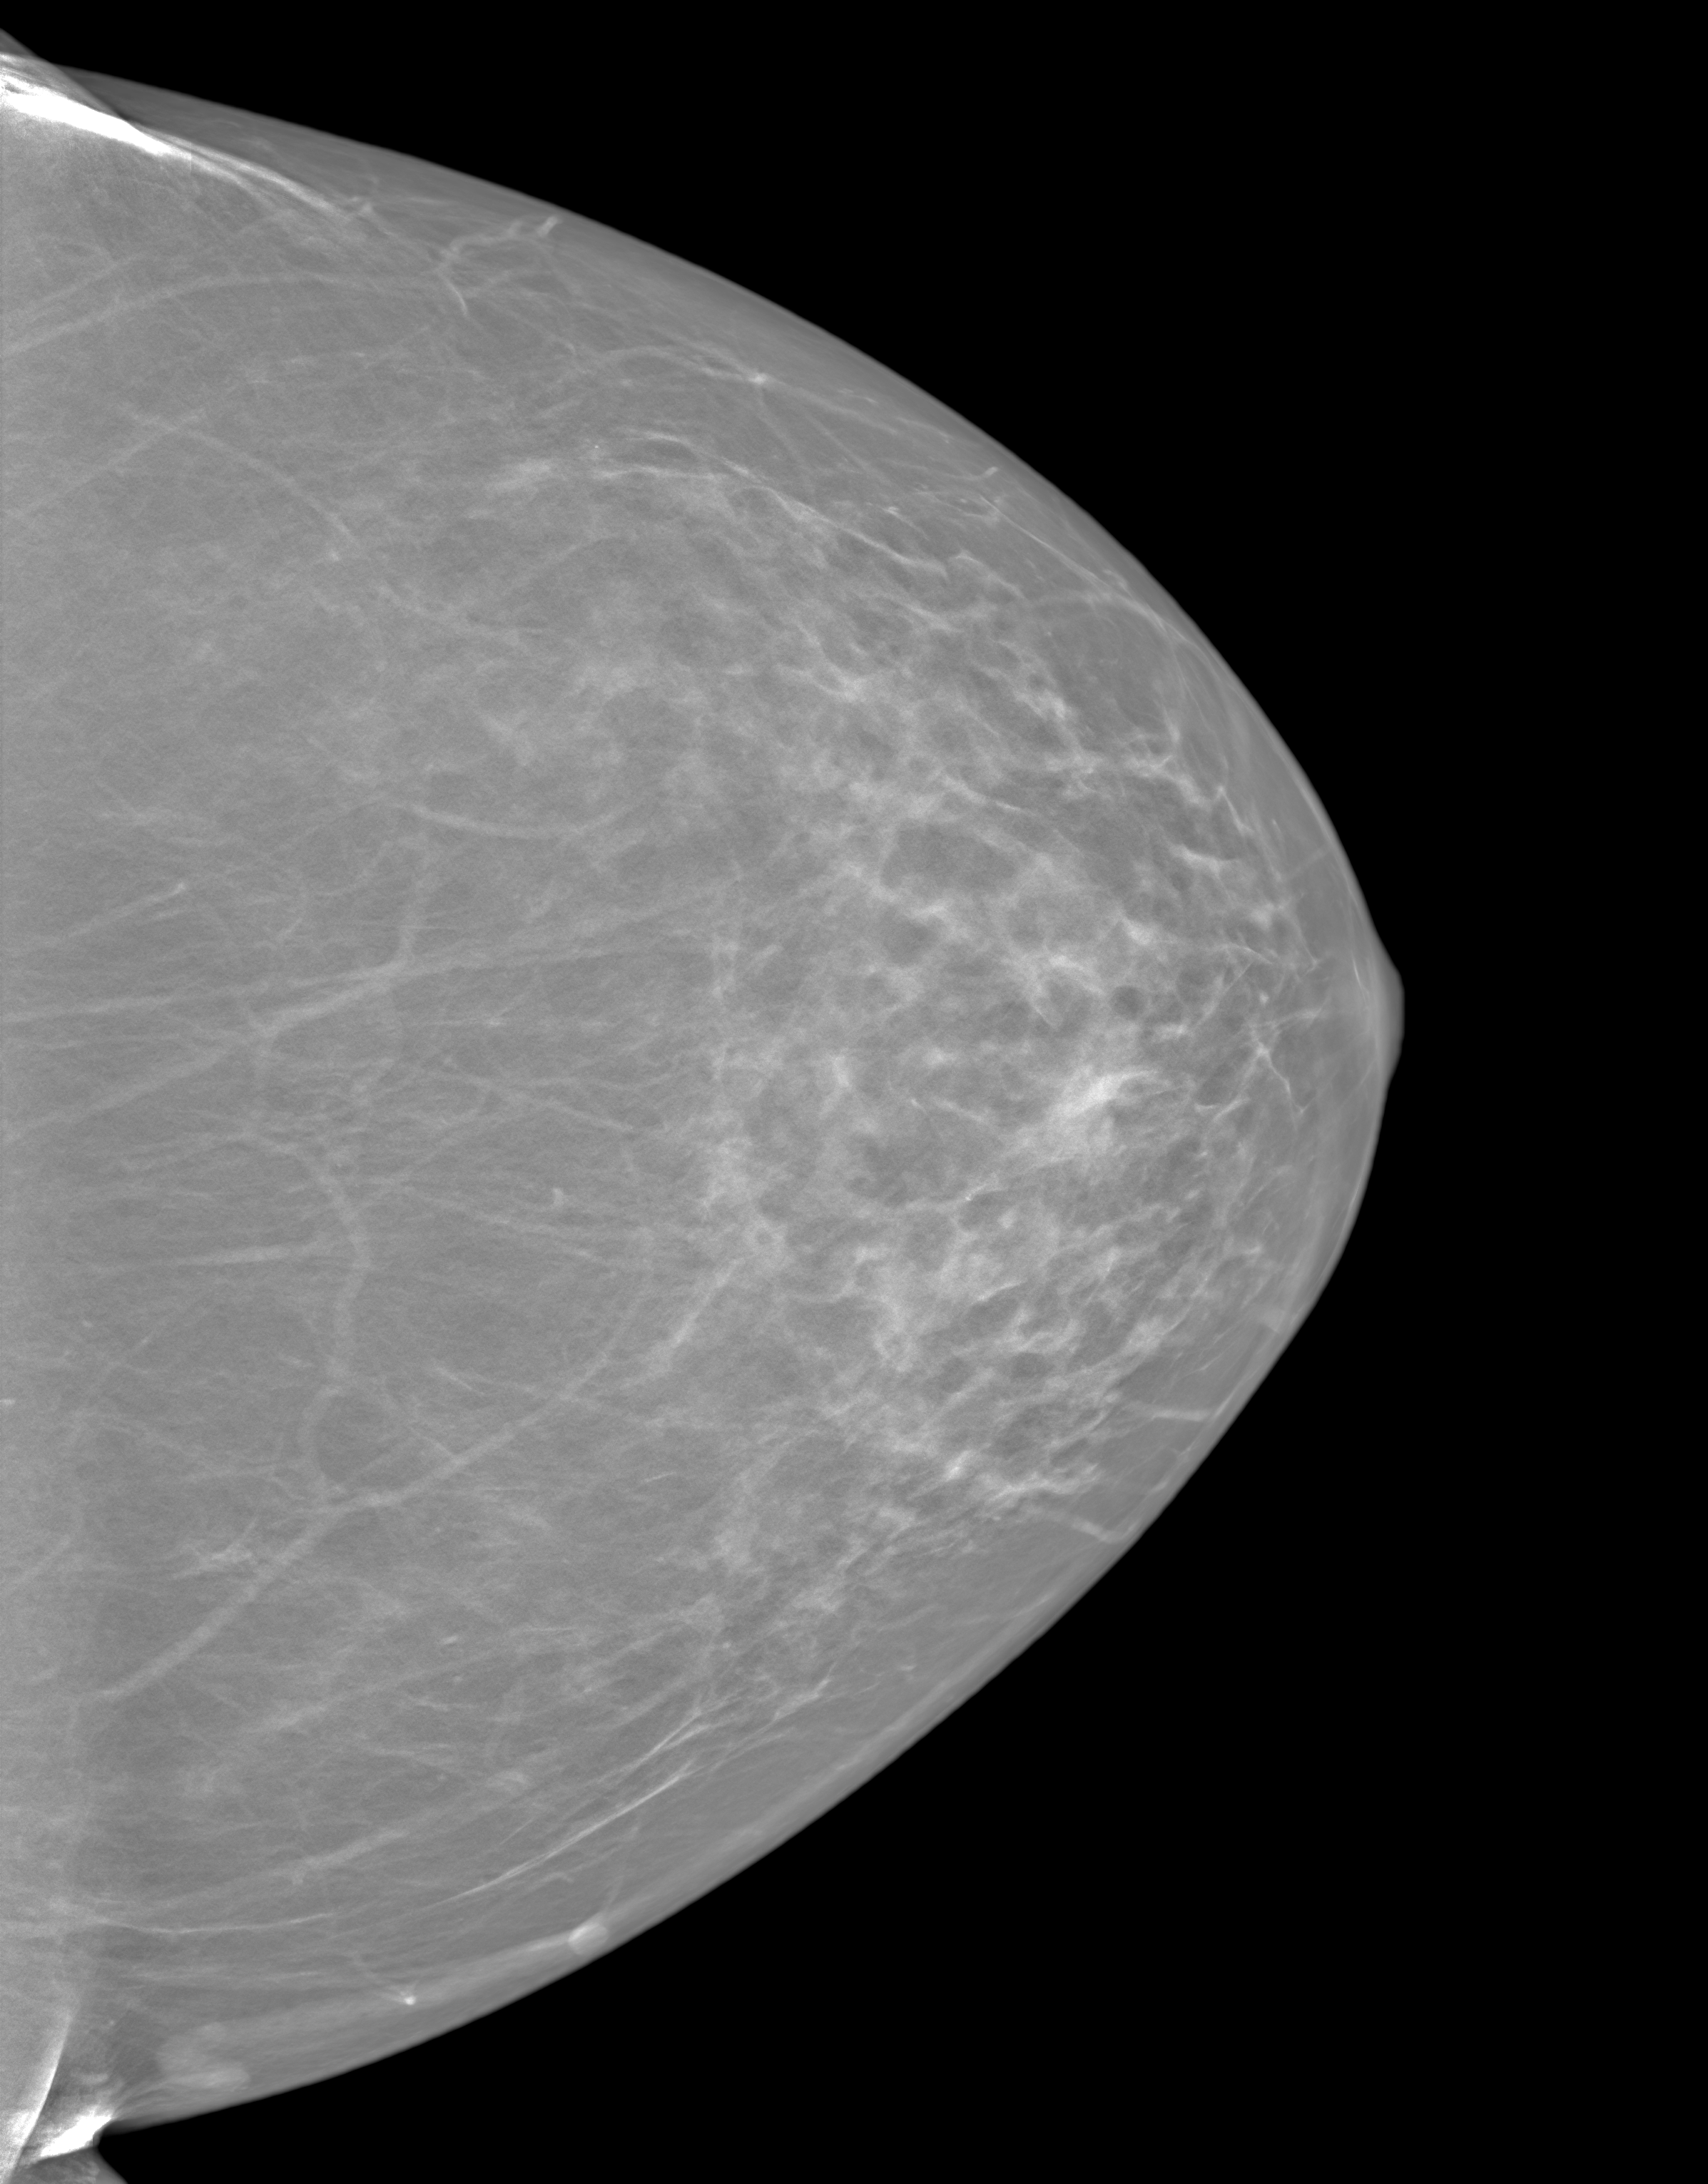
Screening examination. Patient: female, 59 years.
Image type: synthesized 2-D view from tomosynthesis. Breast: left. Projection: cranio-caudal projection.